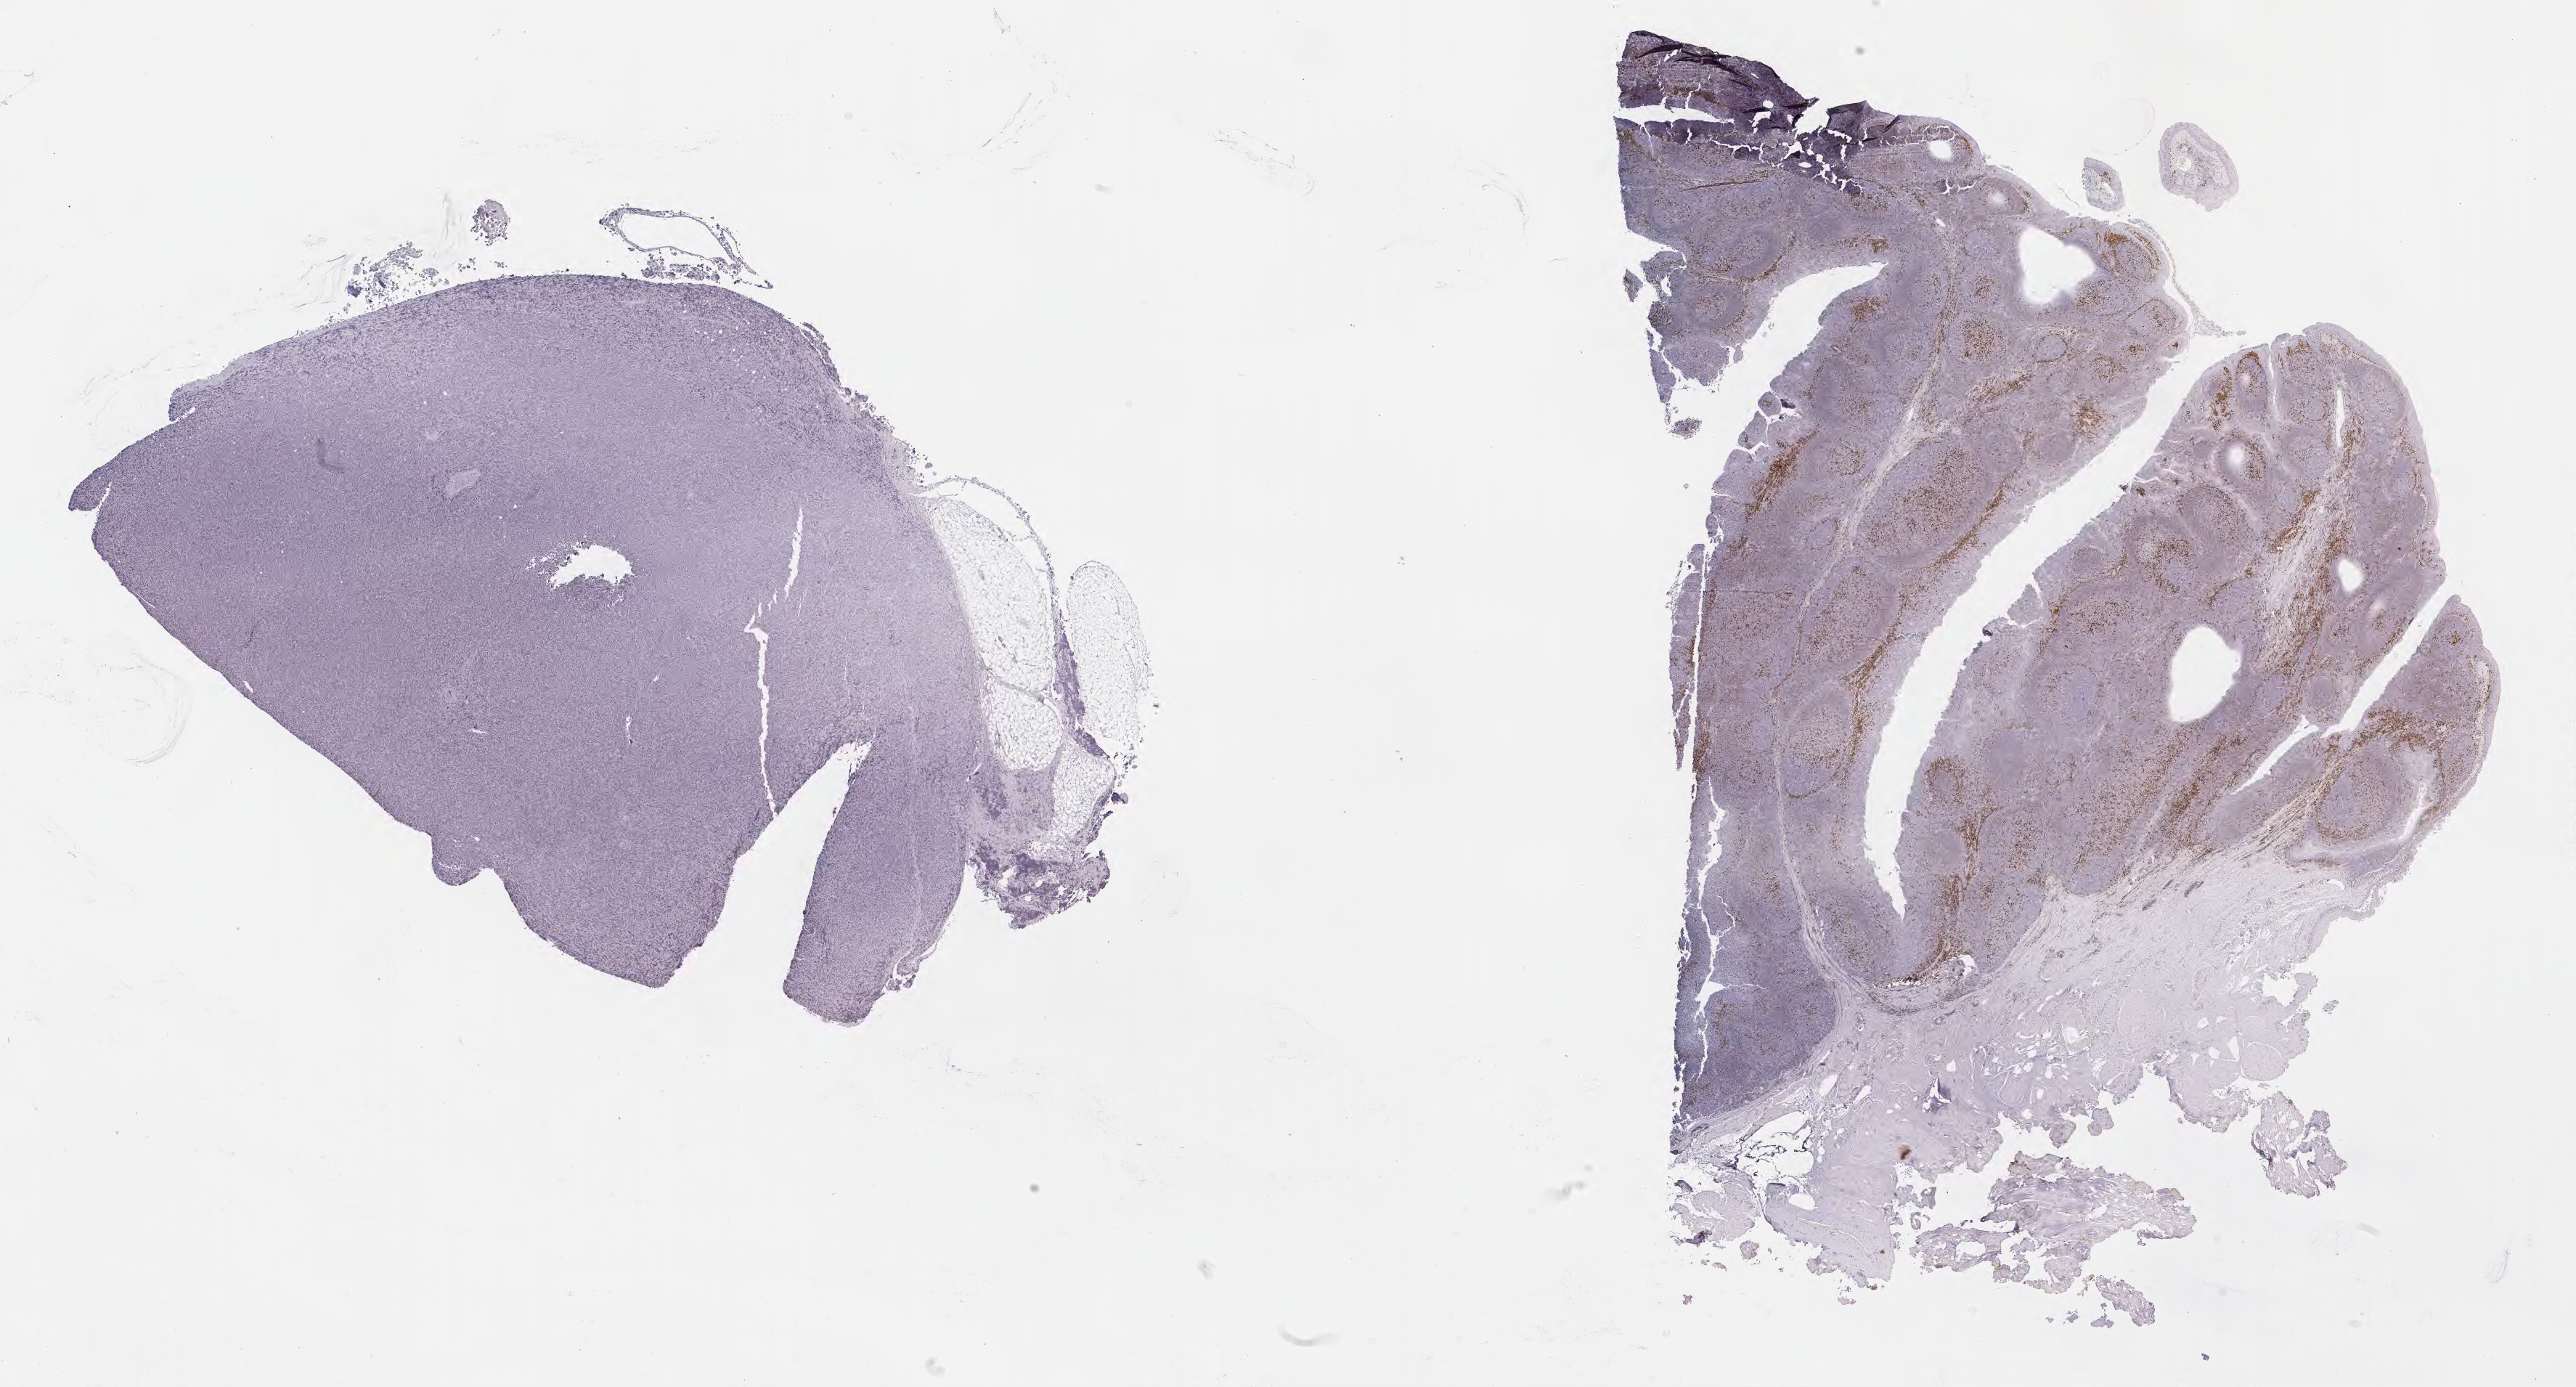
Whole-slide image, immunohistochemical stain for IRF4/MUM1, shown as a low-resolution overview of the whole scanned area (about 28.7 x 15.4 mm), tumor tissue, anatomic site: lymph node. Patient: male, 26 years old.
- histologic diagnosis: Diffuse large B-cell lymphoma, NOS